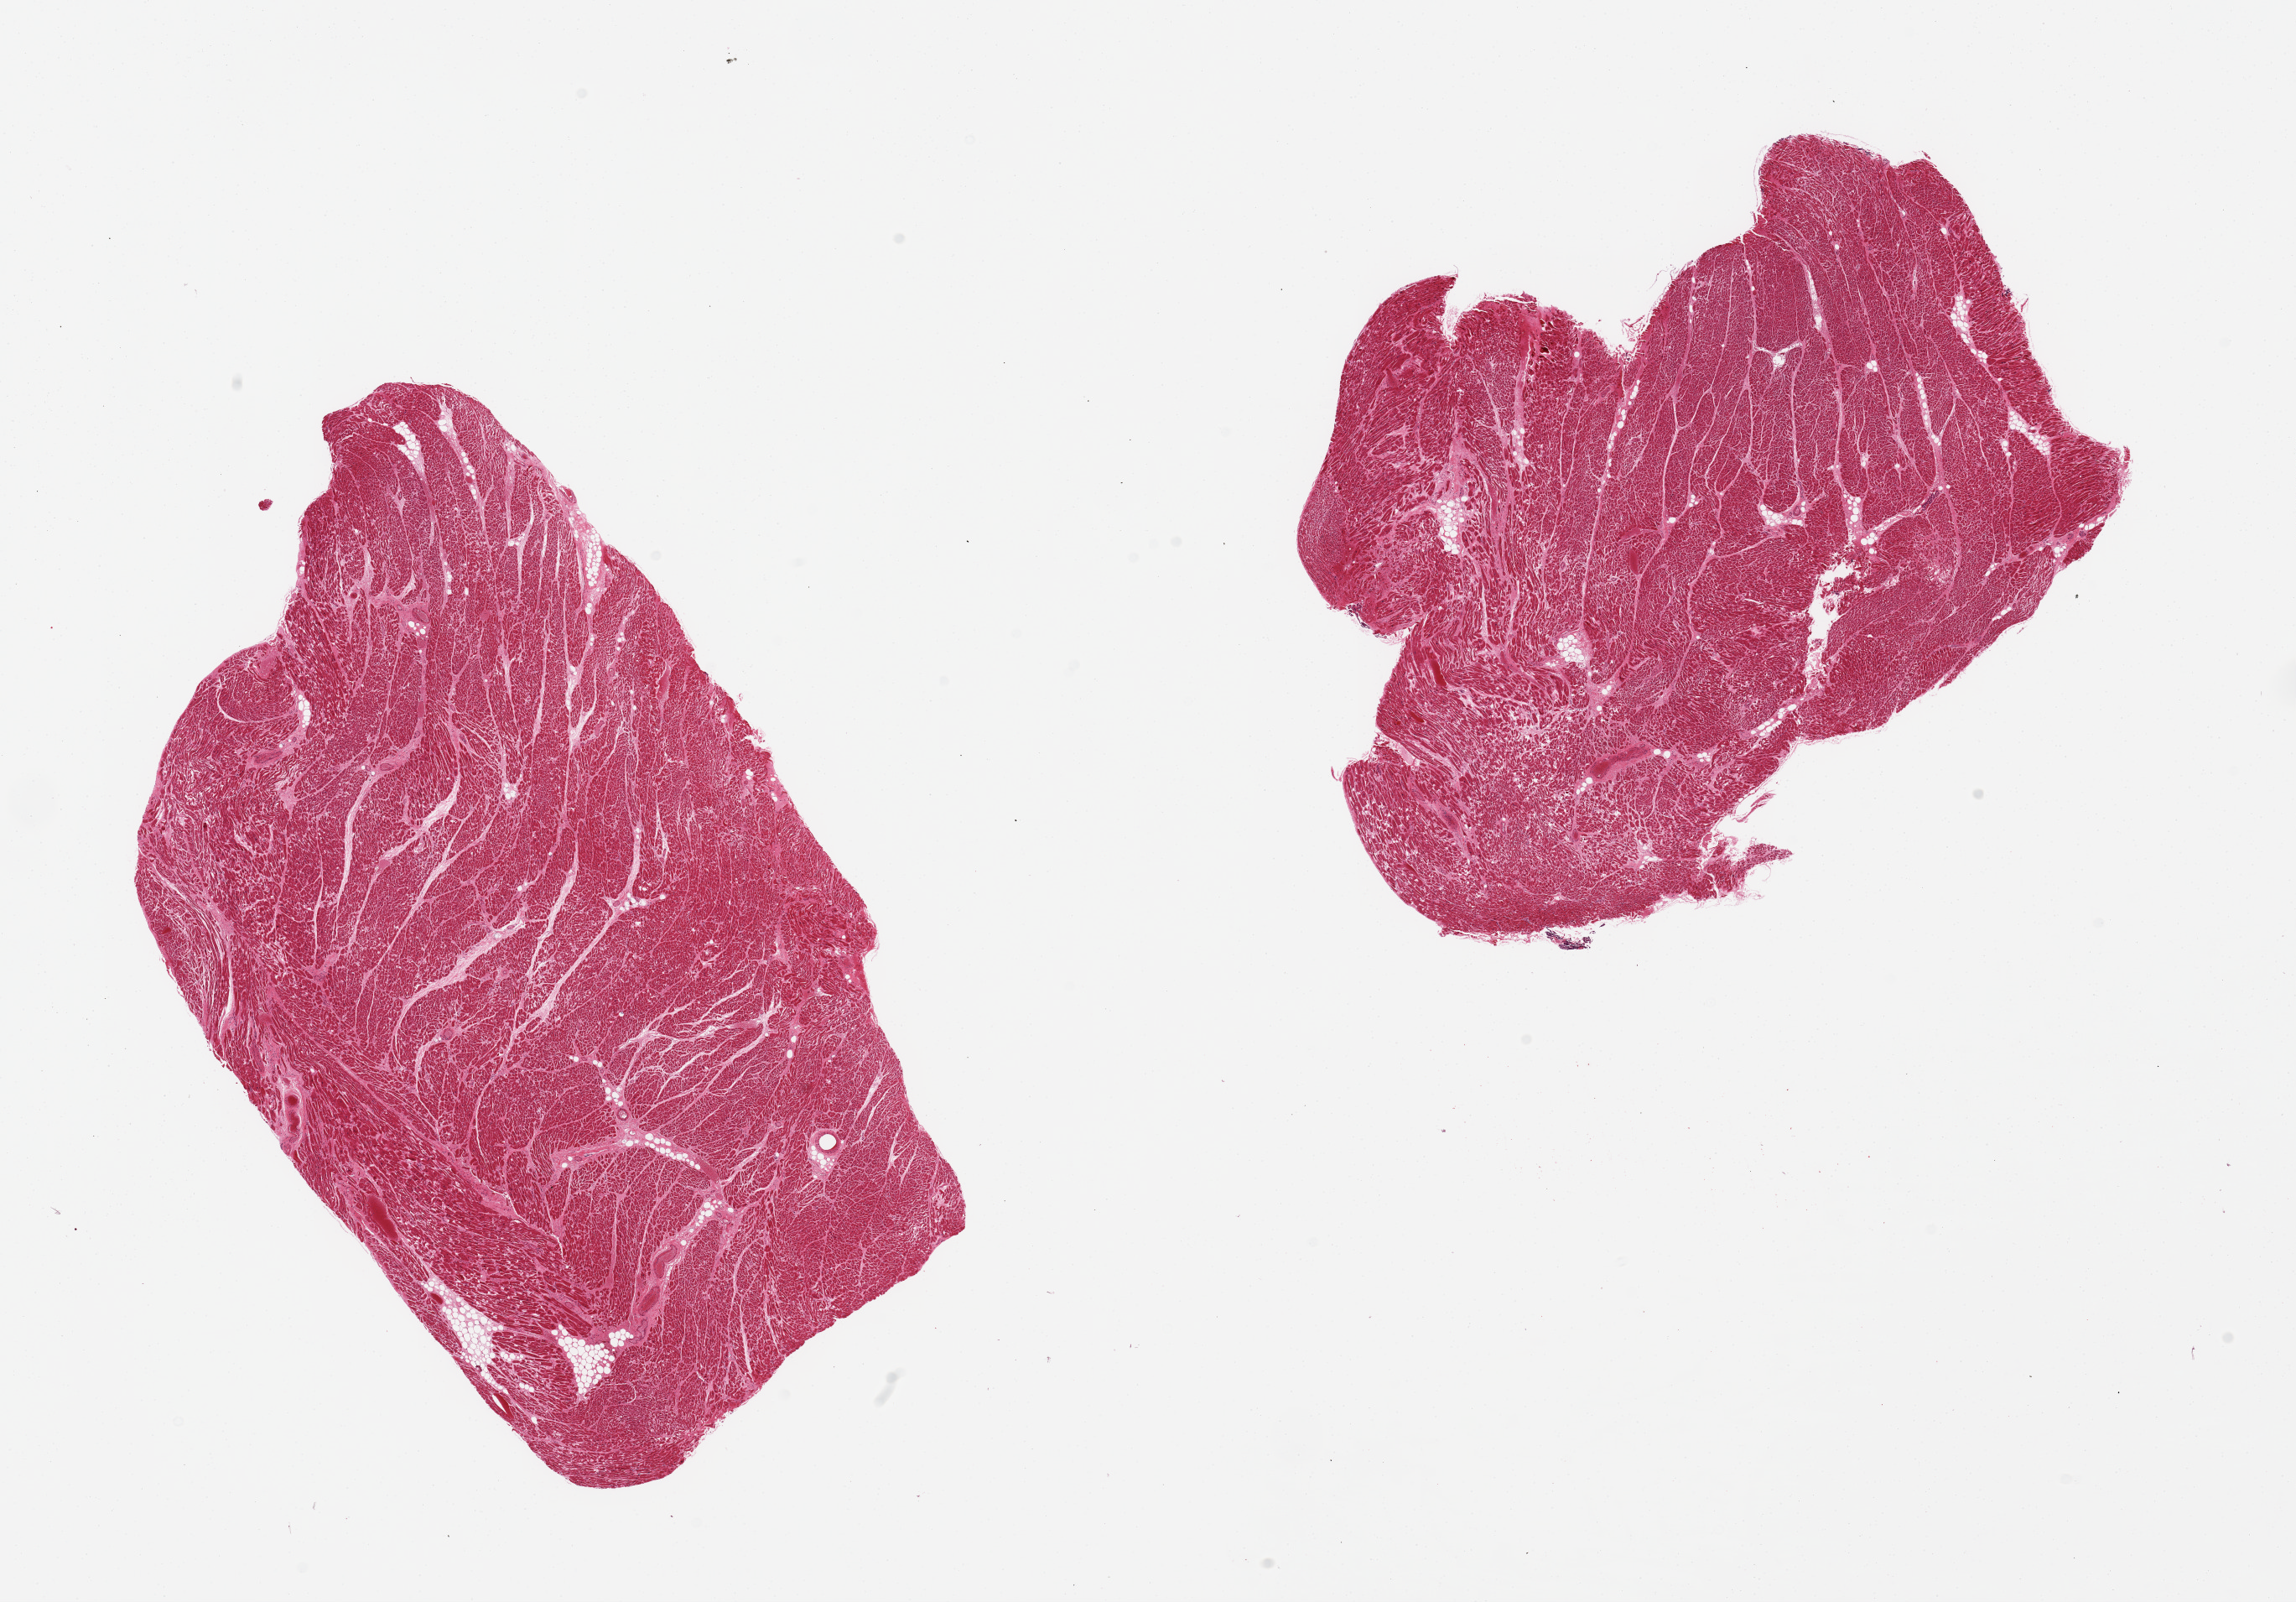
Digitized hematoxylin and eosin (H&E)-stained section, a low-resolution overview of the entire scanned area, about 21.7 x 15.1 mm (acquisition: 20x scan), PAXgene-fixed paraffin-embedded (PFPE) section, sampled site (target tissue): heart, donor tissue sample. Donor sex: male.
- reviewer comment on this tissue sample: 2 pieces, increased interstitial fibrosis, myocyte hypertrophy